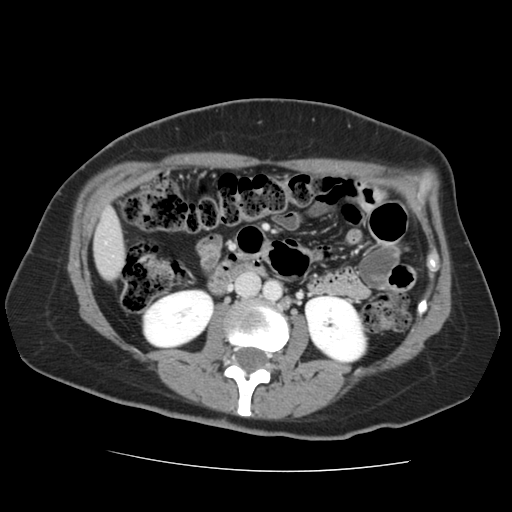
Contrast-enhanced abdominal CT, one axial slice. Position 45 of 144 along the scan axis. Soft-tissue window (W 400 / L 40 HU). 2.5 mm slice thickness. 512 × 512 image matrix, field of view 333 × 333 mm. Female patient, age 46 years. Case-level facts recorded for this patient, not image findings: diagnosis: colorectal cancer liver metastases, imaged before liver resection; multiple liver metastases: no; largest metastasis: 2.8 cm; chemotherapy before resection: yes.
Structures marked on this image (manually delineated by an expert):
- liver: box from (x=94, y=212) to (x=125, y=279) px
- planned liver remnant (the part of the liver to remain after resection): (x=94, y=212)–(x=125, y=262)